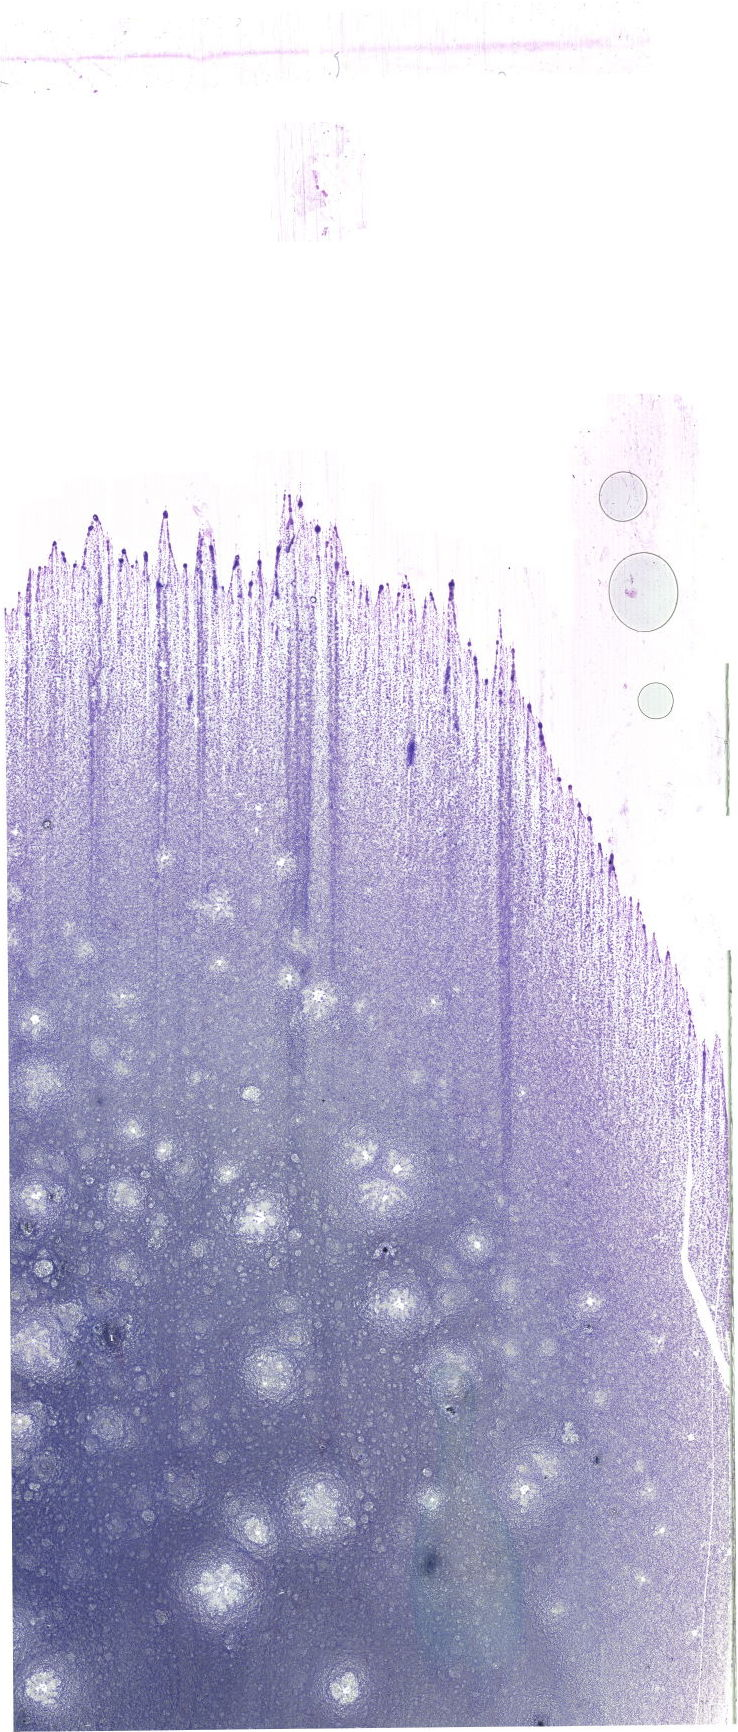
May-Grünwald-Giemsa (MGG)-stained marrow aspirate smear (whole slide), shown as a low-resolution overview of the whole scanned area (about 20.9 x 49.1 mm). Male patient.
• diagnosis: Chronic Phase Chronic Myeloid Leukemia, BCR-ABL1 Positive